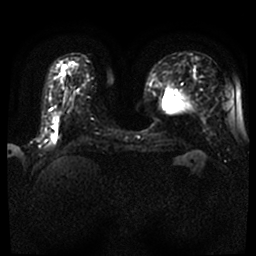
Breast MRI, one axial slice. Slice 14 of 59 in the series (ordered by position). Diffusion-weighted series; image 2 of 4 stored at this slice position (different b-values; order by instance number). 1.5 T. 4 mm slice thickness. 256 × 256 image matrix, field of view 360 × 360 mm. Female patient.
Annotated regions visible in this slice (expert manual segmentation):
- tumour on diffusion-weighted imaging: box from (x=54, y=126) to (x=58, y=136) px